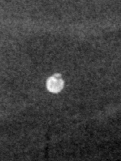
Cropped region of a digitized screen-film mammogram centred on a radiologist-marked abnormality; left breast; CC view; BI-RADS breast density category 1 (scale 1–4).
- Finding: calcifications, morphology lucent centered; BI-RADS assessment category 2; benign; no additional work-up was recommended (benign without callback).